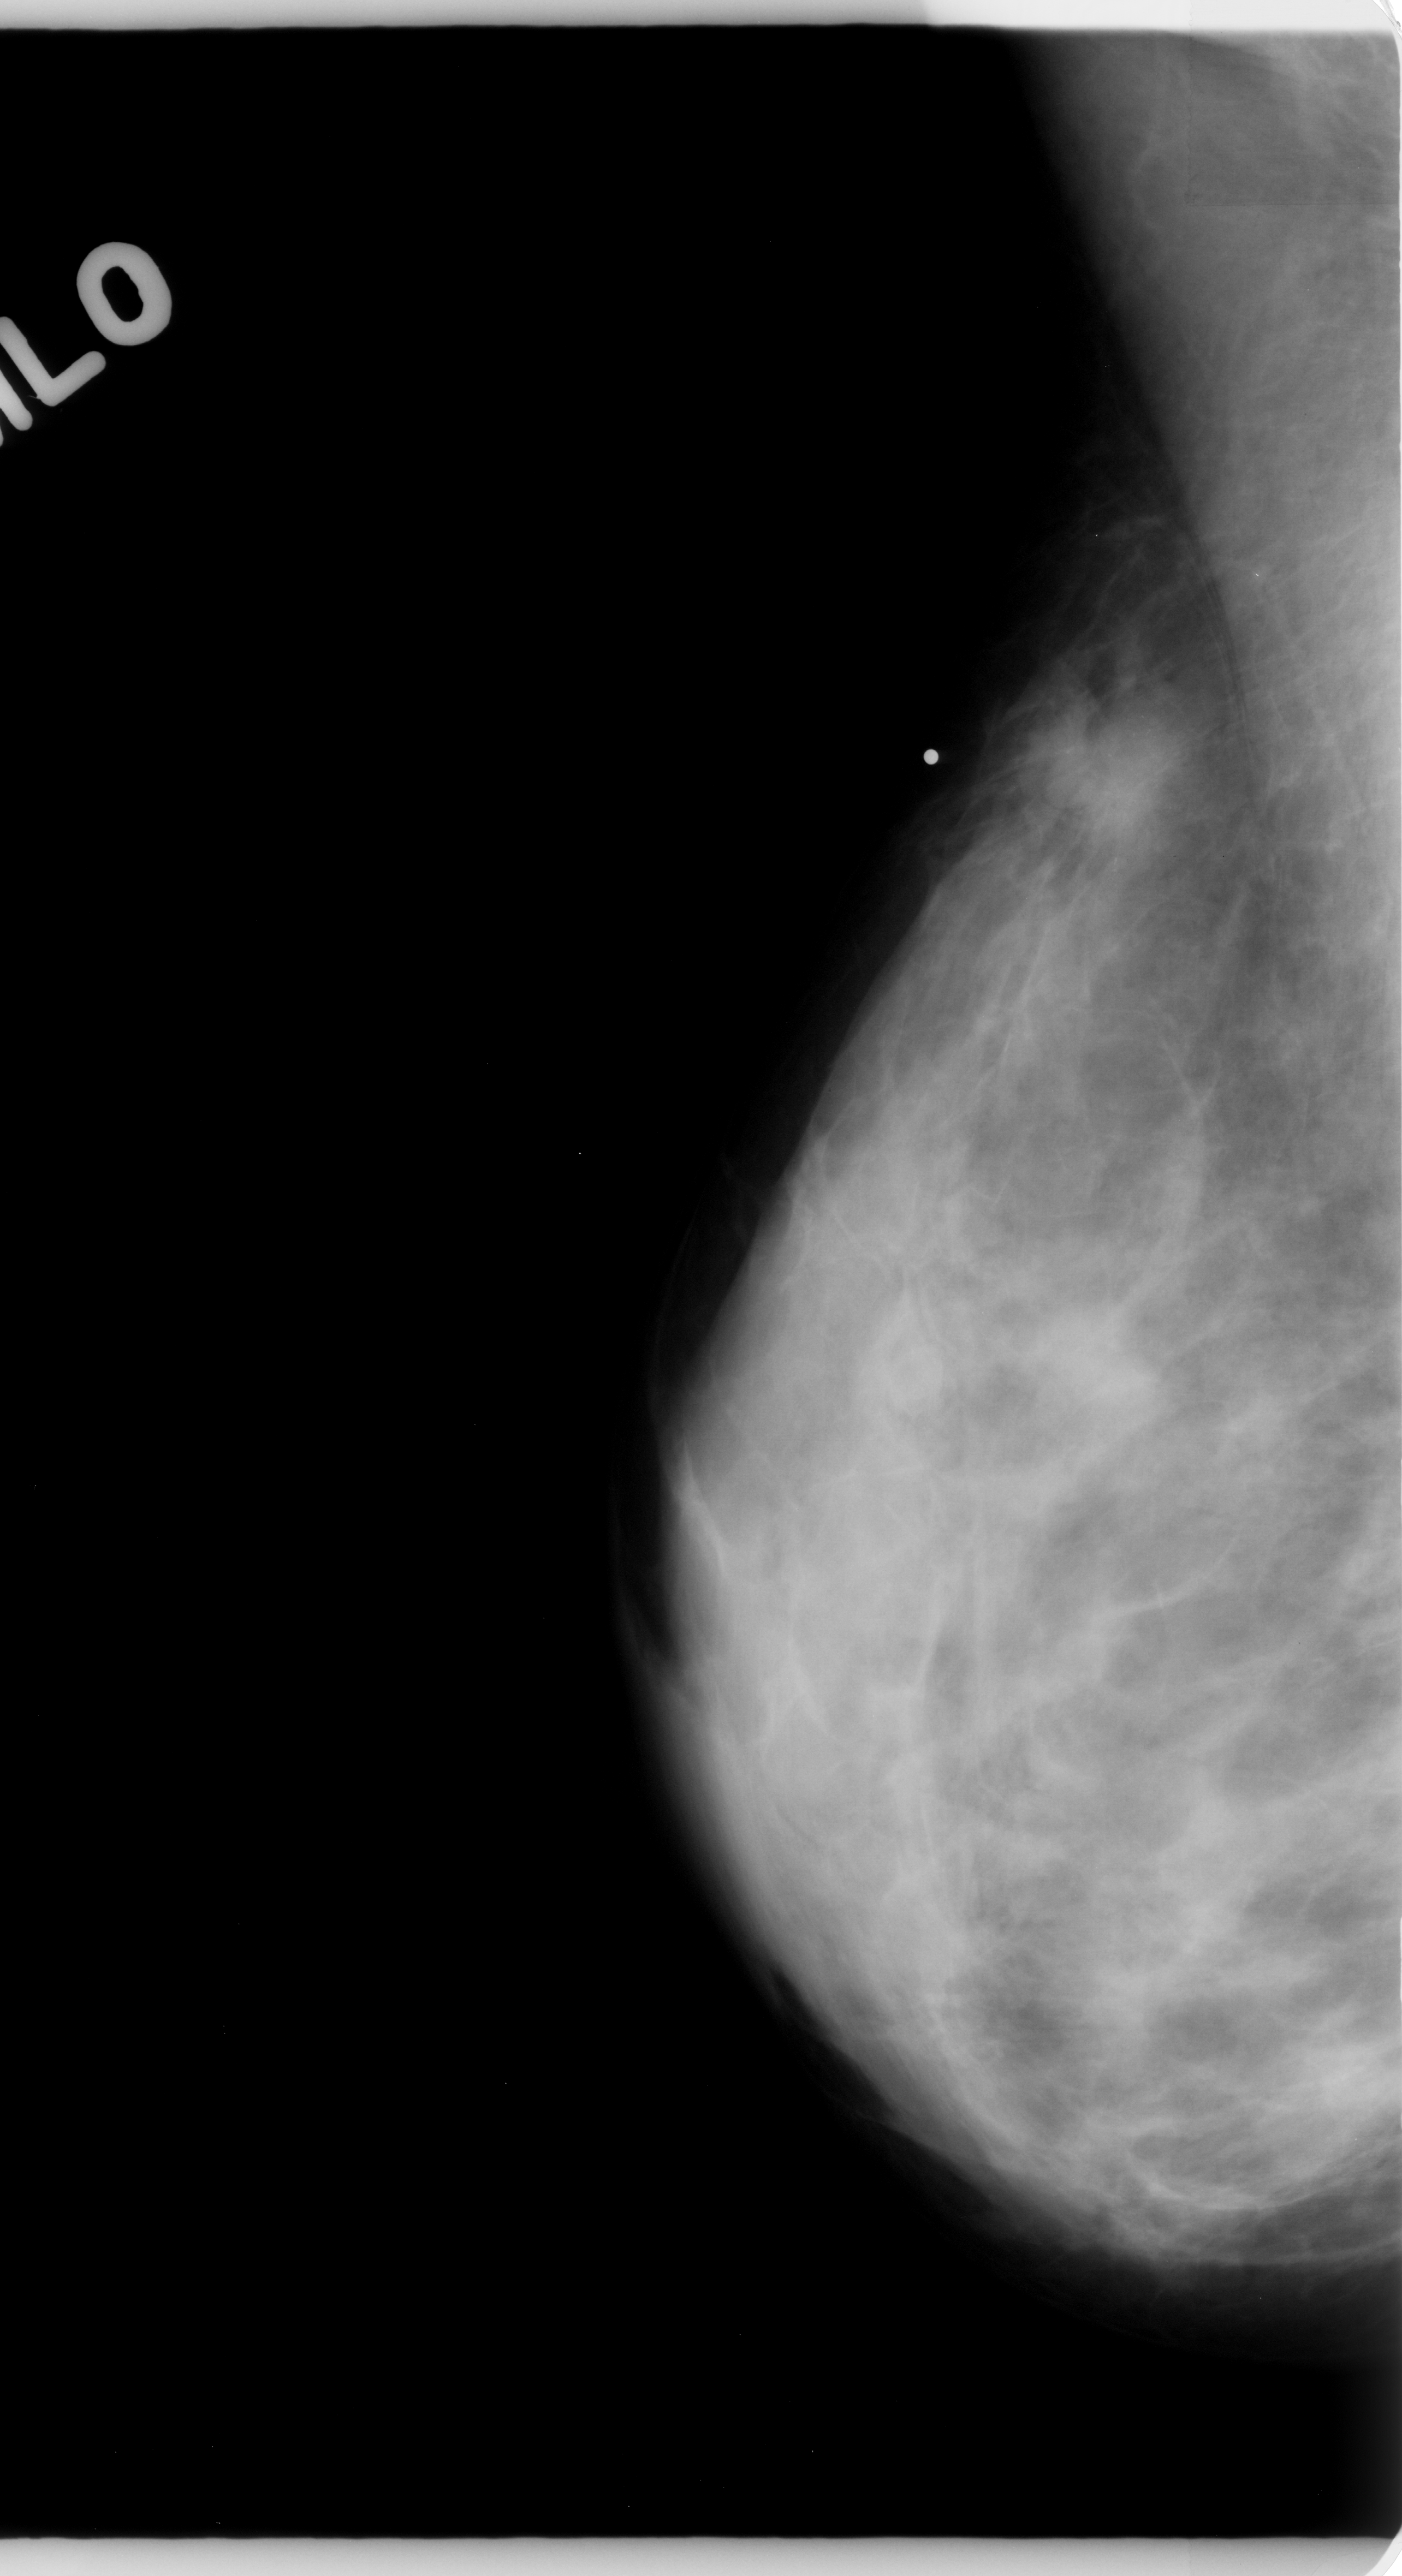
Digitized screen-film mammogram; right breast; MLO view; BI-RADS breast density category 3 (scale 1–4).
- Mass, shape irregular, margins spiculated; BI-RADS assessment category 5; pathology (as recorded): malignant.